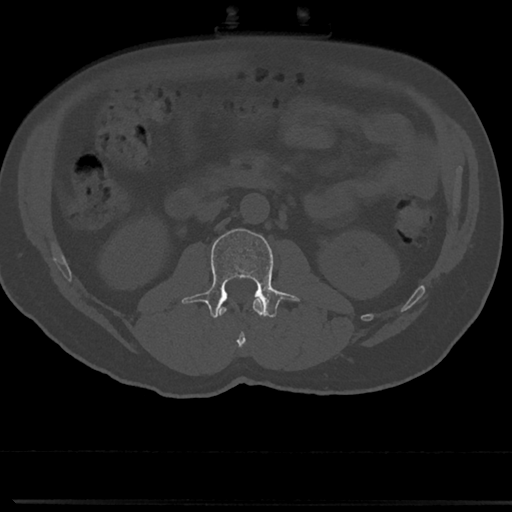
CT including the spine, one axial slice. Position 28 of 817 along the scan axis. Reconstruction kernel Br40s/3. Bone window (W 1800 / L 400 HU). 0.5 mm slice thickness. 512 × 512 image matrix, field of view 355 × 355 mm. Male patient, age 61 years. Case-level facts recorded for this patient, not image findings: primary cancer: prostate.
Structures marked on this image (semi-automatic segmentation, software-assisted and operator-edited):
- L1 vertebra: bounding box [x1, y1, x2, y2] px = [219, 298, 263, 350]
- L2 vertebra: [191, 228, 297, 319]